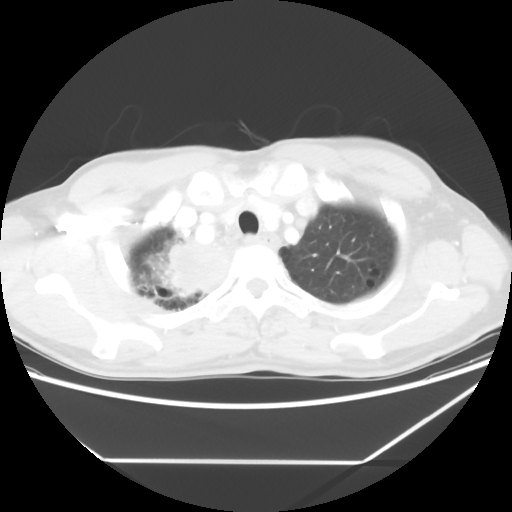
Chest CT, one axial slice. Slice 53 of 60 in the series (ordered by position). 120 kVp. Lung window (W 1500 / L -600 HU). 512 × 512 image matrix. Patient: male, 58 years. From the clinical record (not read from this slice): clinical TNM (as recorded): T2 N2 M0.
Outlined on this slice (rectangle marked by the reading radiologist):
- lung tumour (recorded histology: squamous cell carcinoma): bounding box [x1, y1, x2, y2] px = [157, 234, 232, 302]